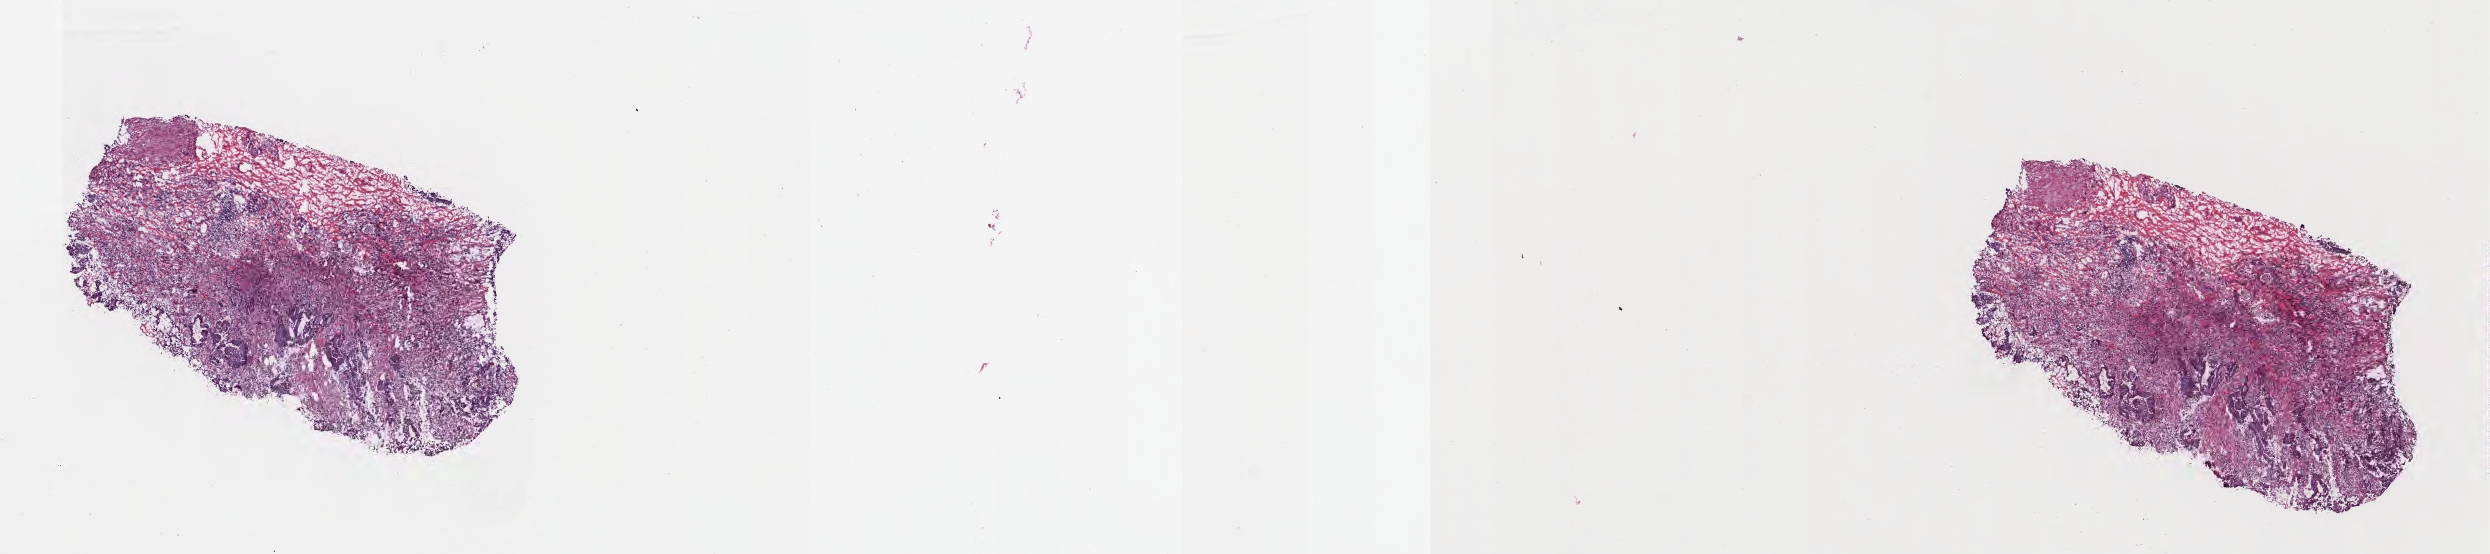
Whole-slide image, H&E stain, a low-resolution overview of the entire scanned area, about 20.1 x 4.5 mm, cryosection, metastatic tumor tissue. Patient: female, age at initial diagnosis 63 years. Pathologist review of this section (percent, as recorded): tumor cells 20%, tumor nuclei 20%, stromal cells 60%, necrosis 0%, normal cells 20%. Inflammatory infiltration, as recorded: lymphocyte infiltration 15%, monocyte infiltration 1%, neutrophil infiltration 4%.
Patient diagnosis (primary): Adenocarcinoma, NOS.